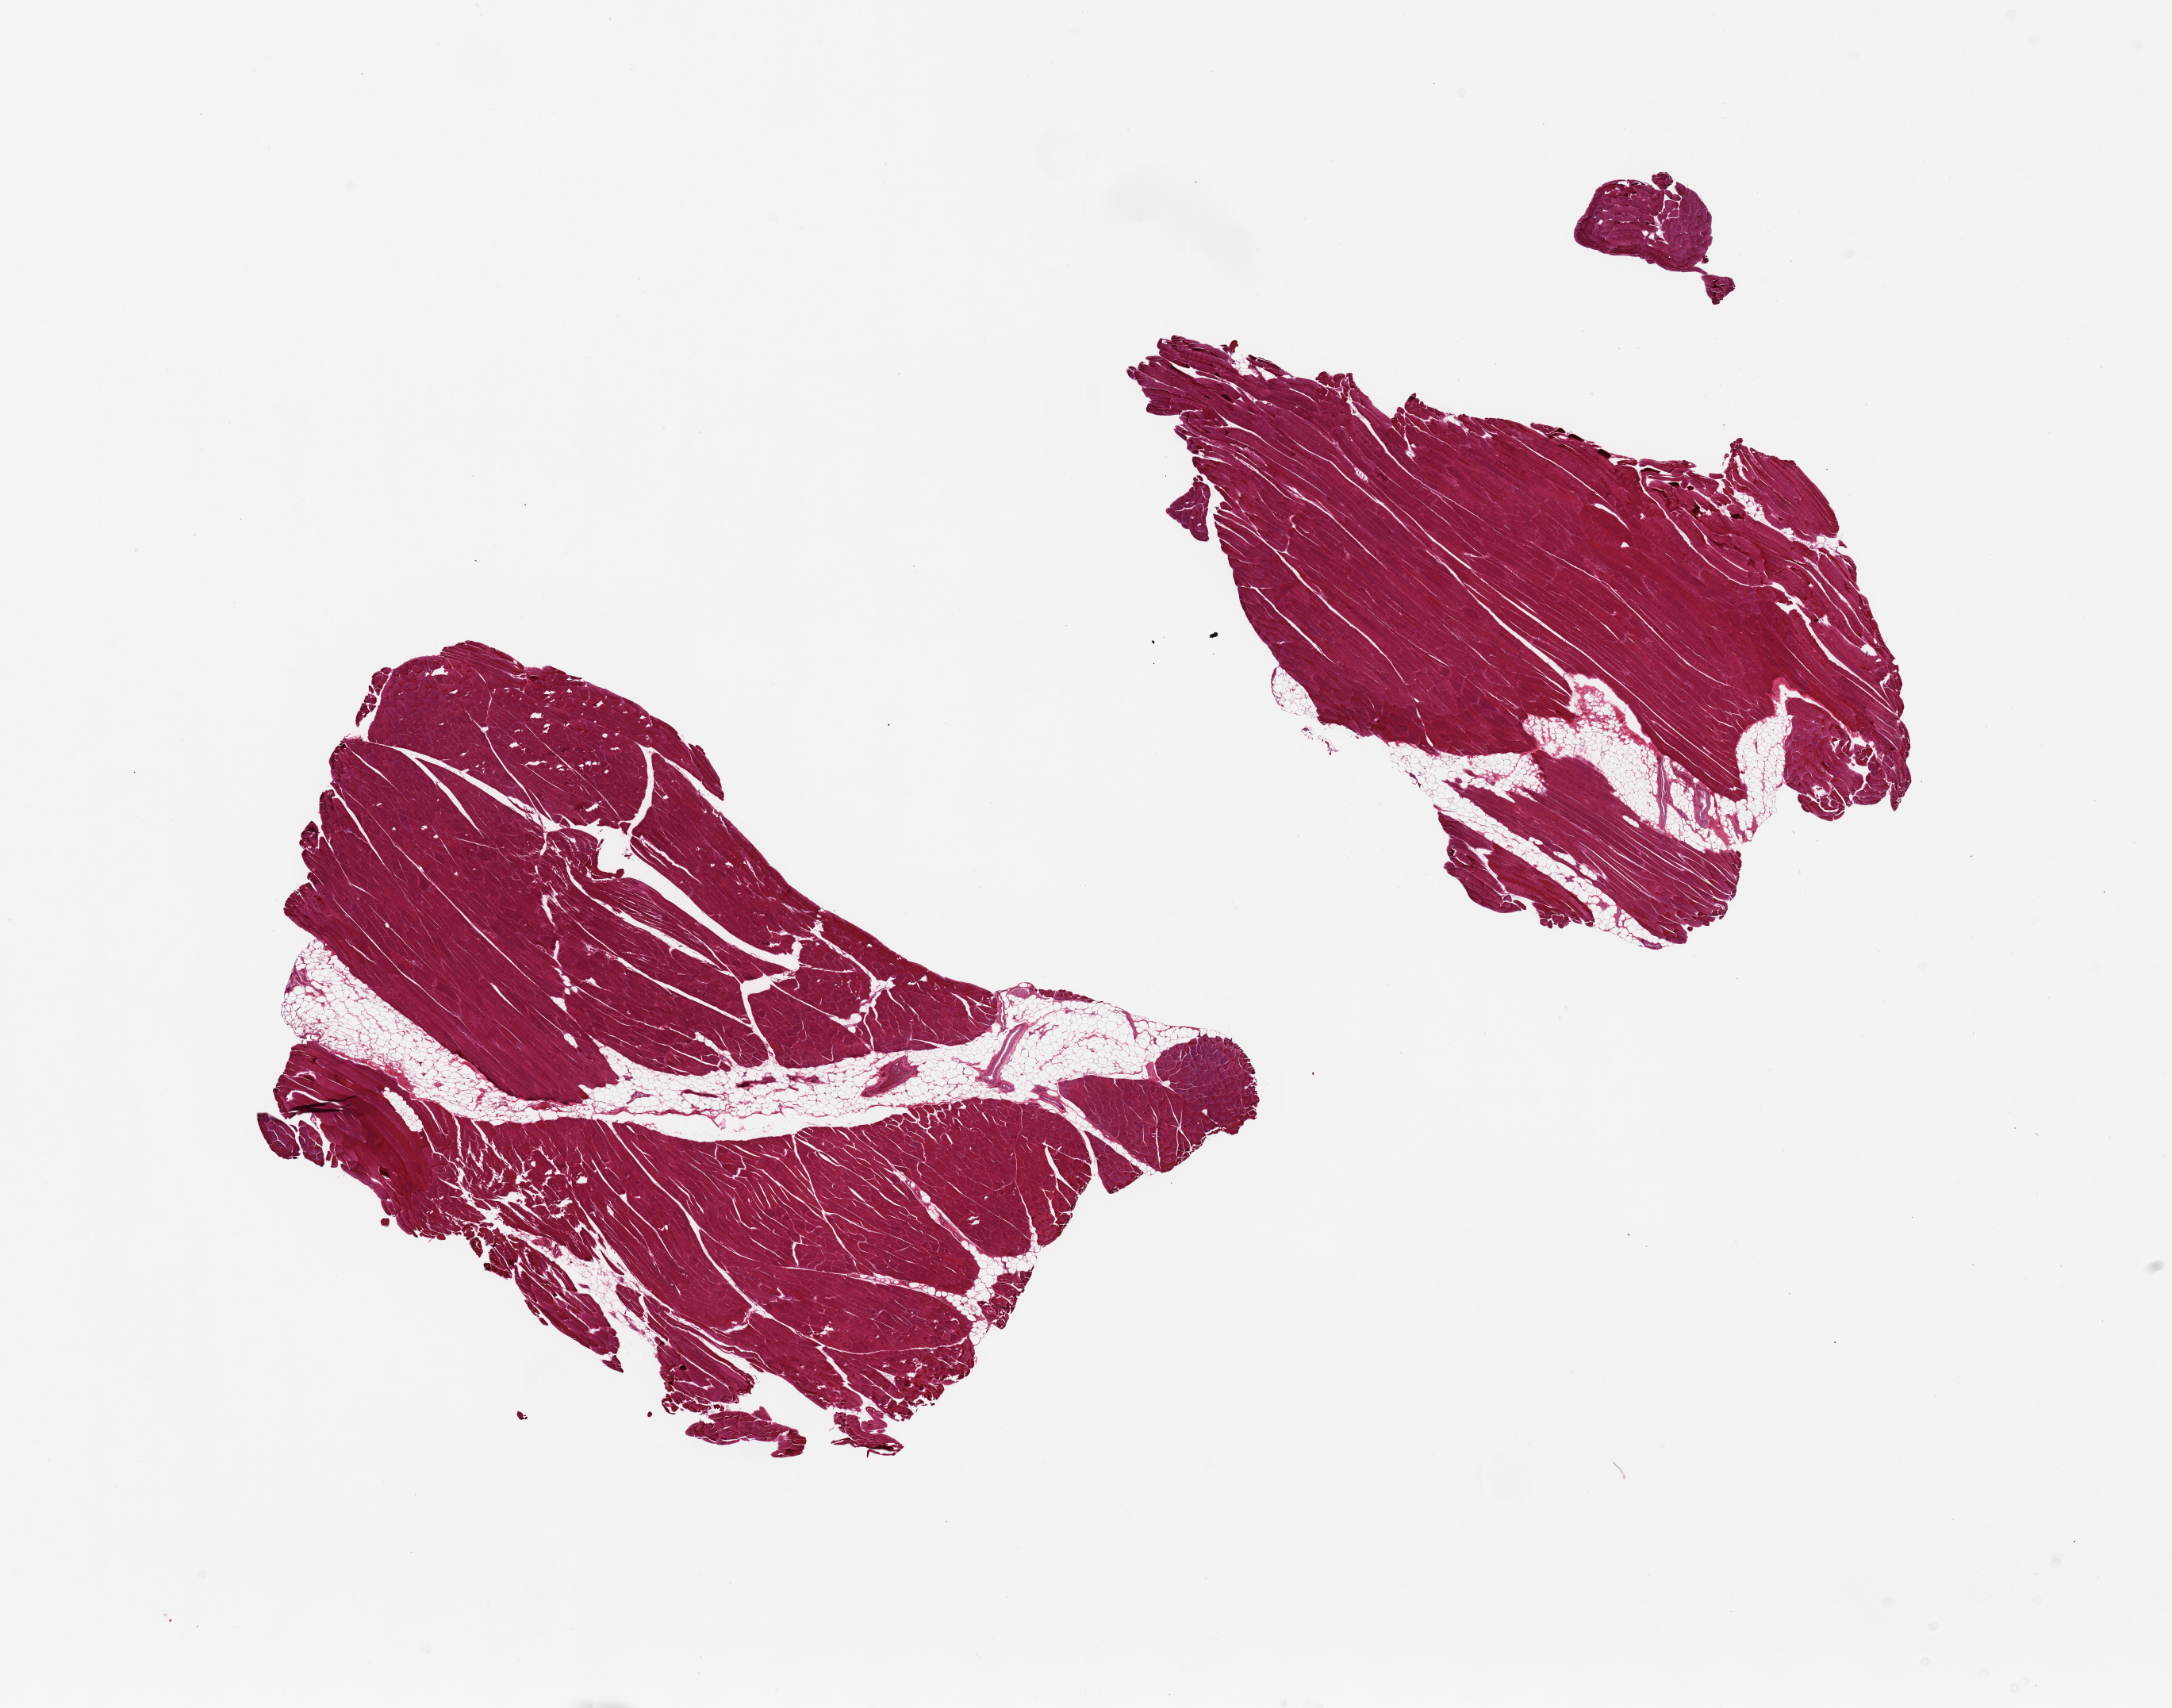
Hematoxylin and eosin (H&E) whole-slide image, whole scanned area (about 21.7 x 17.0 mm) shown as a low-resolution overview, PAXgene-fixed paraffin-embedded (PFPE) section, sampled site (target tissue): skeletal muscle, tissue donor sample. Male donor.
Review note (as recorded): 2 pieces 9 x 5 and 8 x 5 mm. 10% internal adipose.